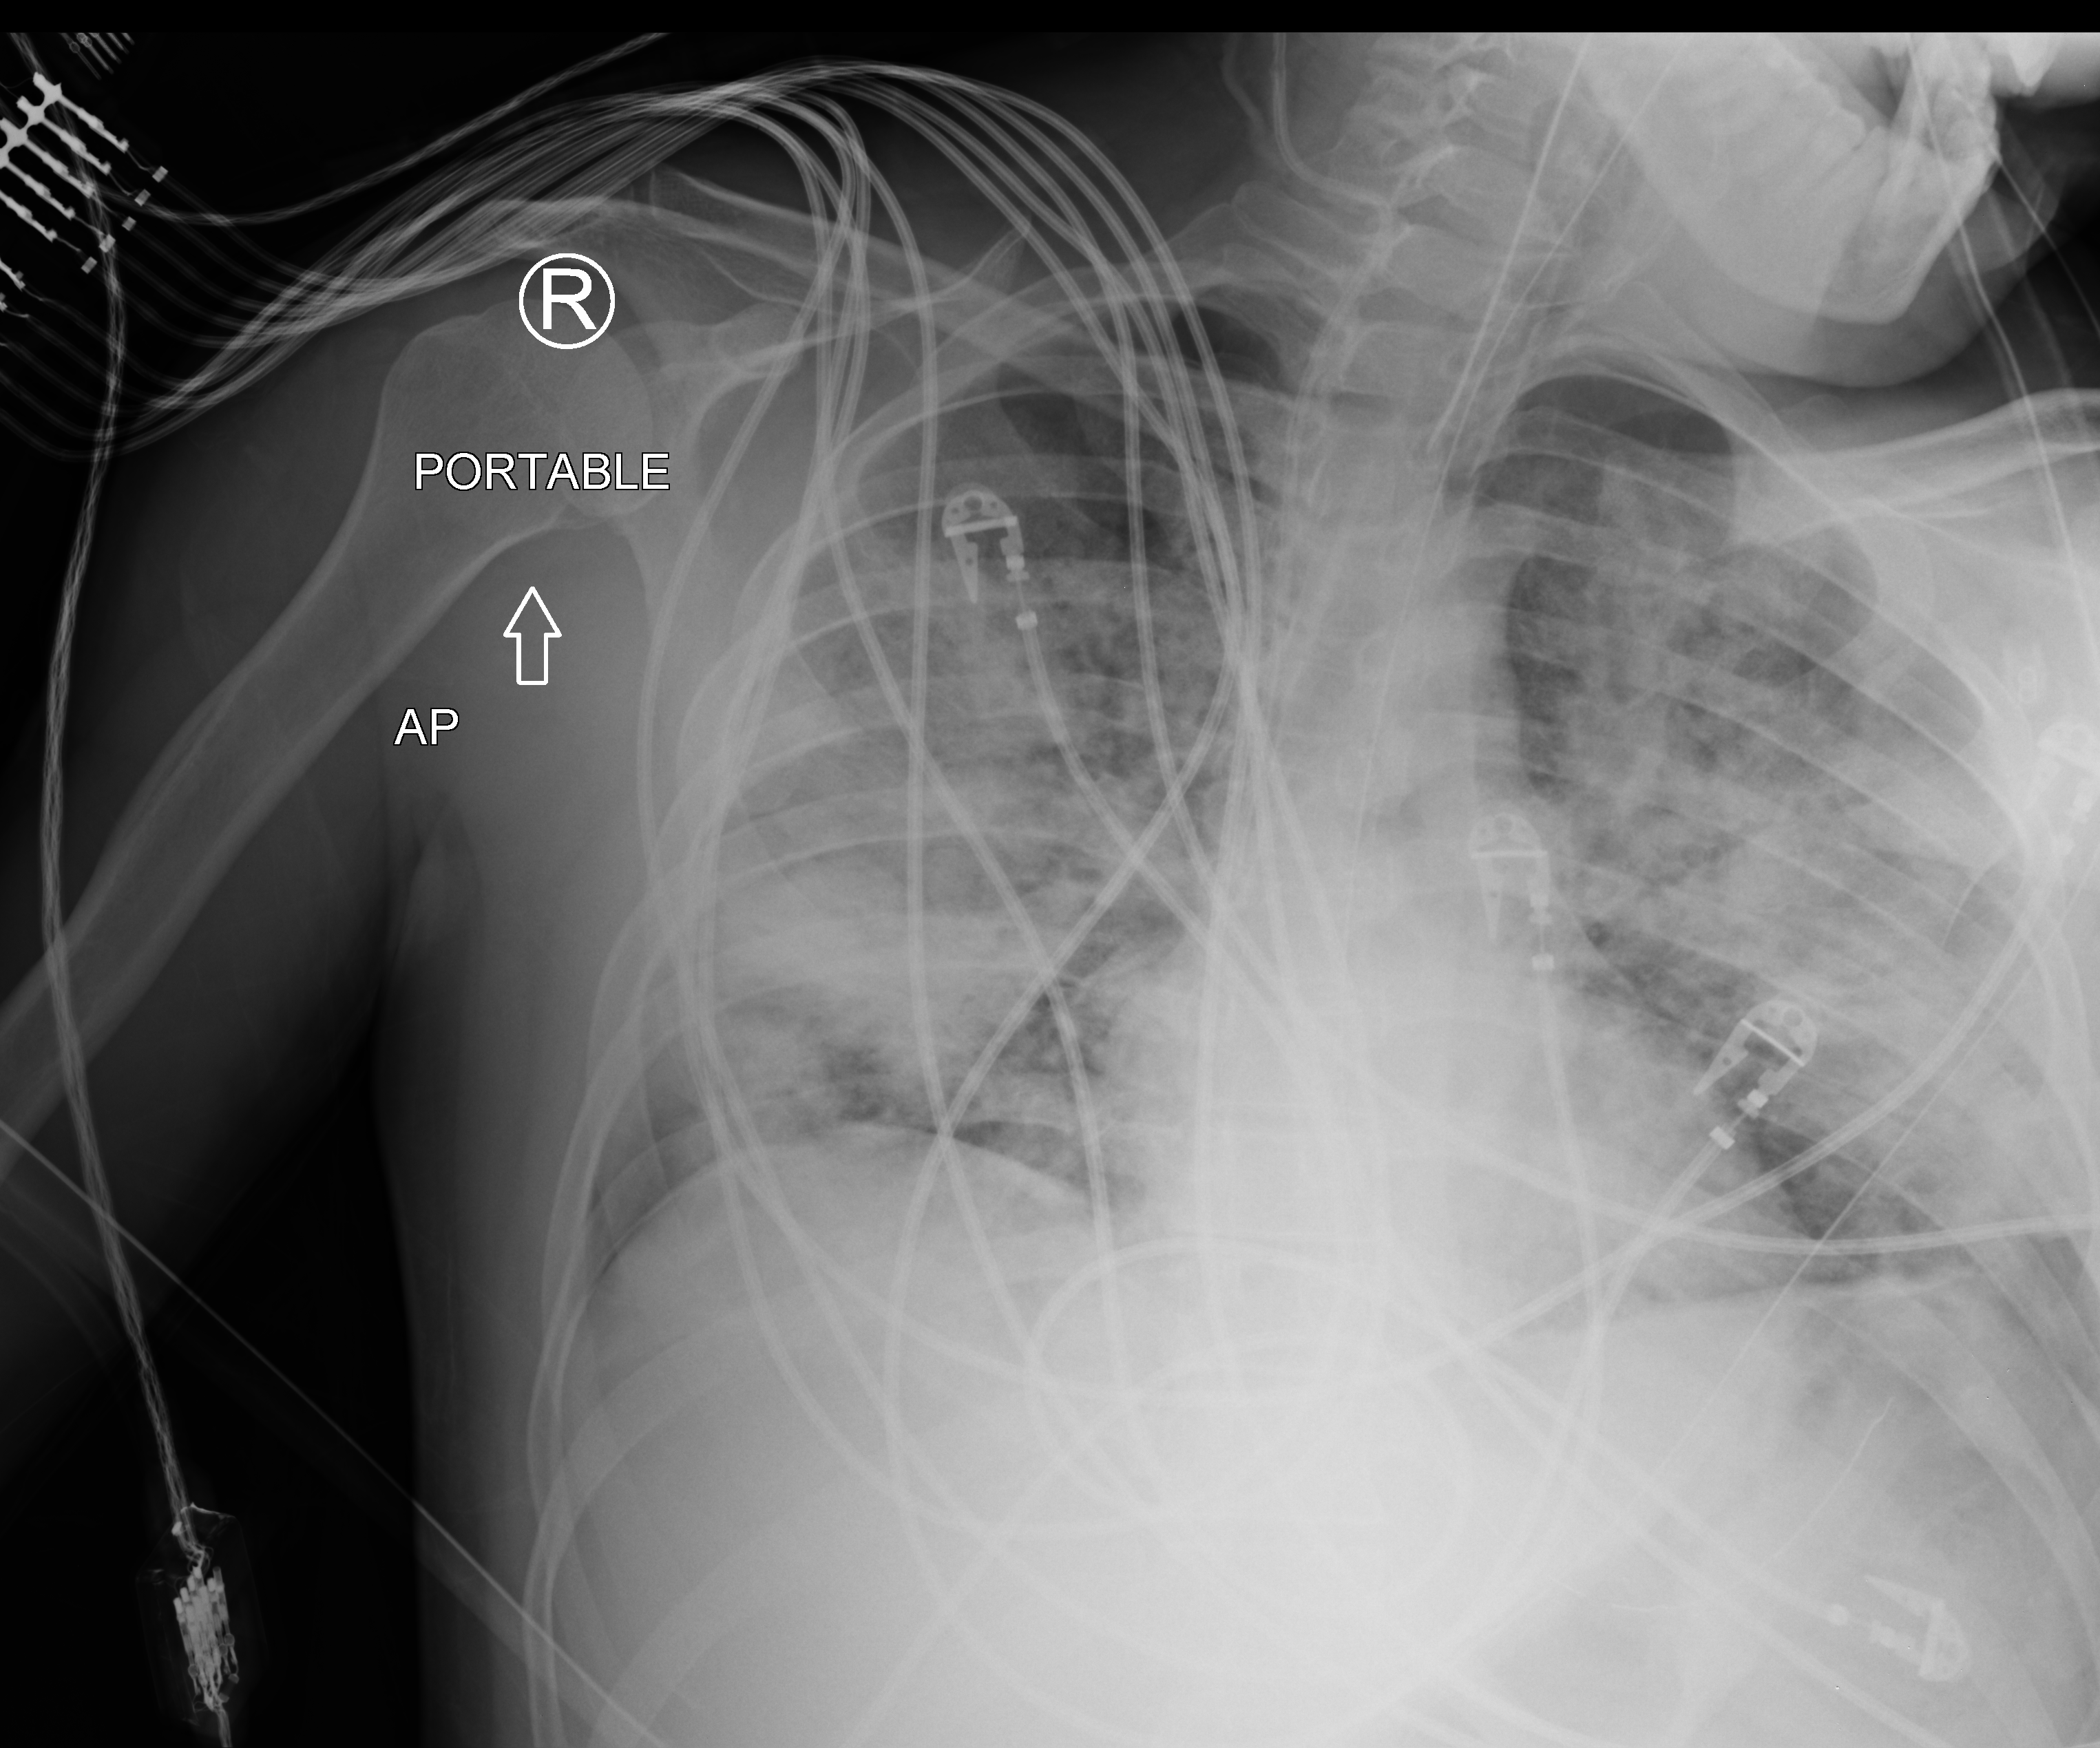
Chest X-ray (portable), anteroposterior (AP) projection. Male patient hospitalised with COVID-19, age 18–59 years.
From the hospital-stay record, not from the radiograph (when in the stay this image was taken is not recorded):
- length of hospital stay: 29 days
- mechanically ventilated during this hospital stay: yes
- COPD (admission record): no